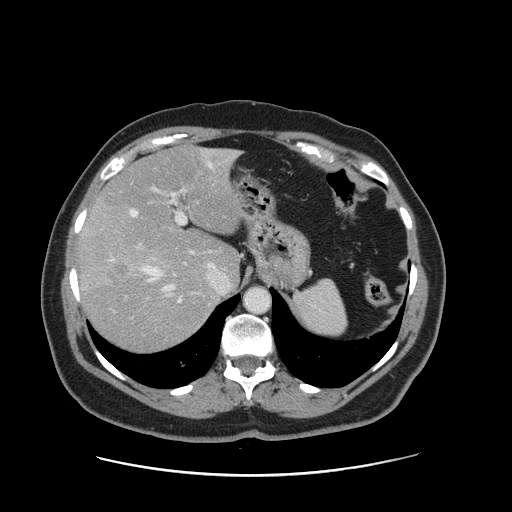
Contrast-enhanced abdominal CT, one axial slice. Slice 110 of 161 in the series (ordered by position). 120 kVp. Intravenous contrast given. Soft-tissue window (W 400 / L 40 HU). 2.5 mm slice thickness. 512 × 512 image matrix, field of view 398 × 398 mm. Female patient, age 62 years. From the clinical record (not read from this slice): diagnosis: colorectal cancer liver metastases, imaged before liver resection; multiple liver metastases: no; largest metastasis: 2.5 cm.
Structures marked on this image (expert manual segmentation):
- hepatic veins: bounding box [x1, y1, x2, y2] px = [131, 152, 237, 291]
- liver: [80, 147, 240, 353]
- planned liver remnant (the part of the liver to remain after resection): [99, 148, 239, 280]
- portal vein (with intrahepatic branches): [113, 186, 188, 313]
- liver metastasis: [107, 263, 131, 289]